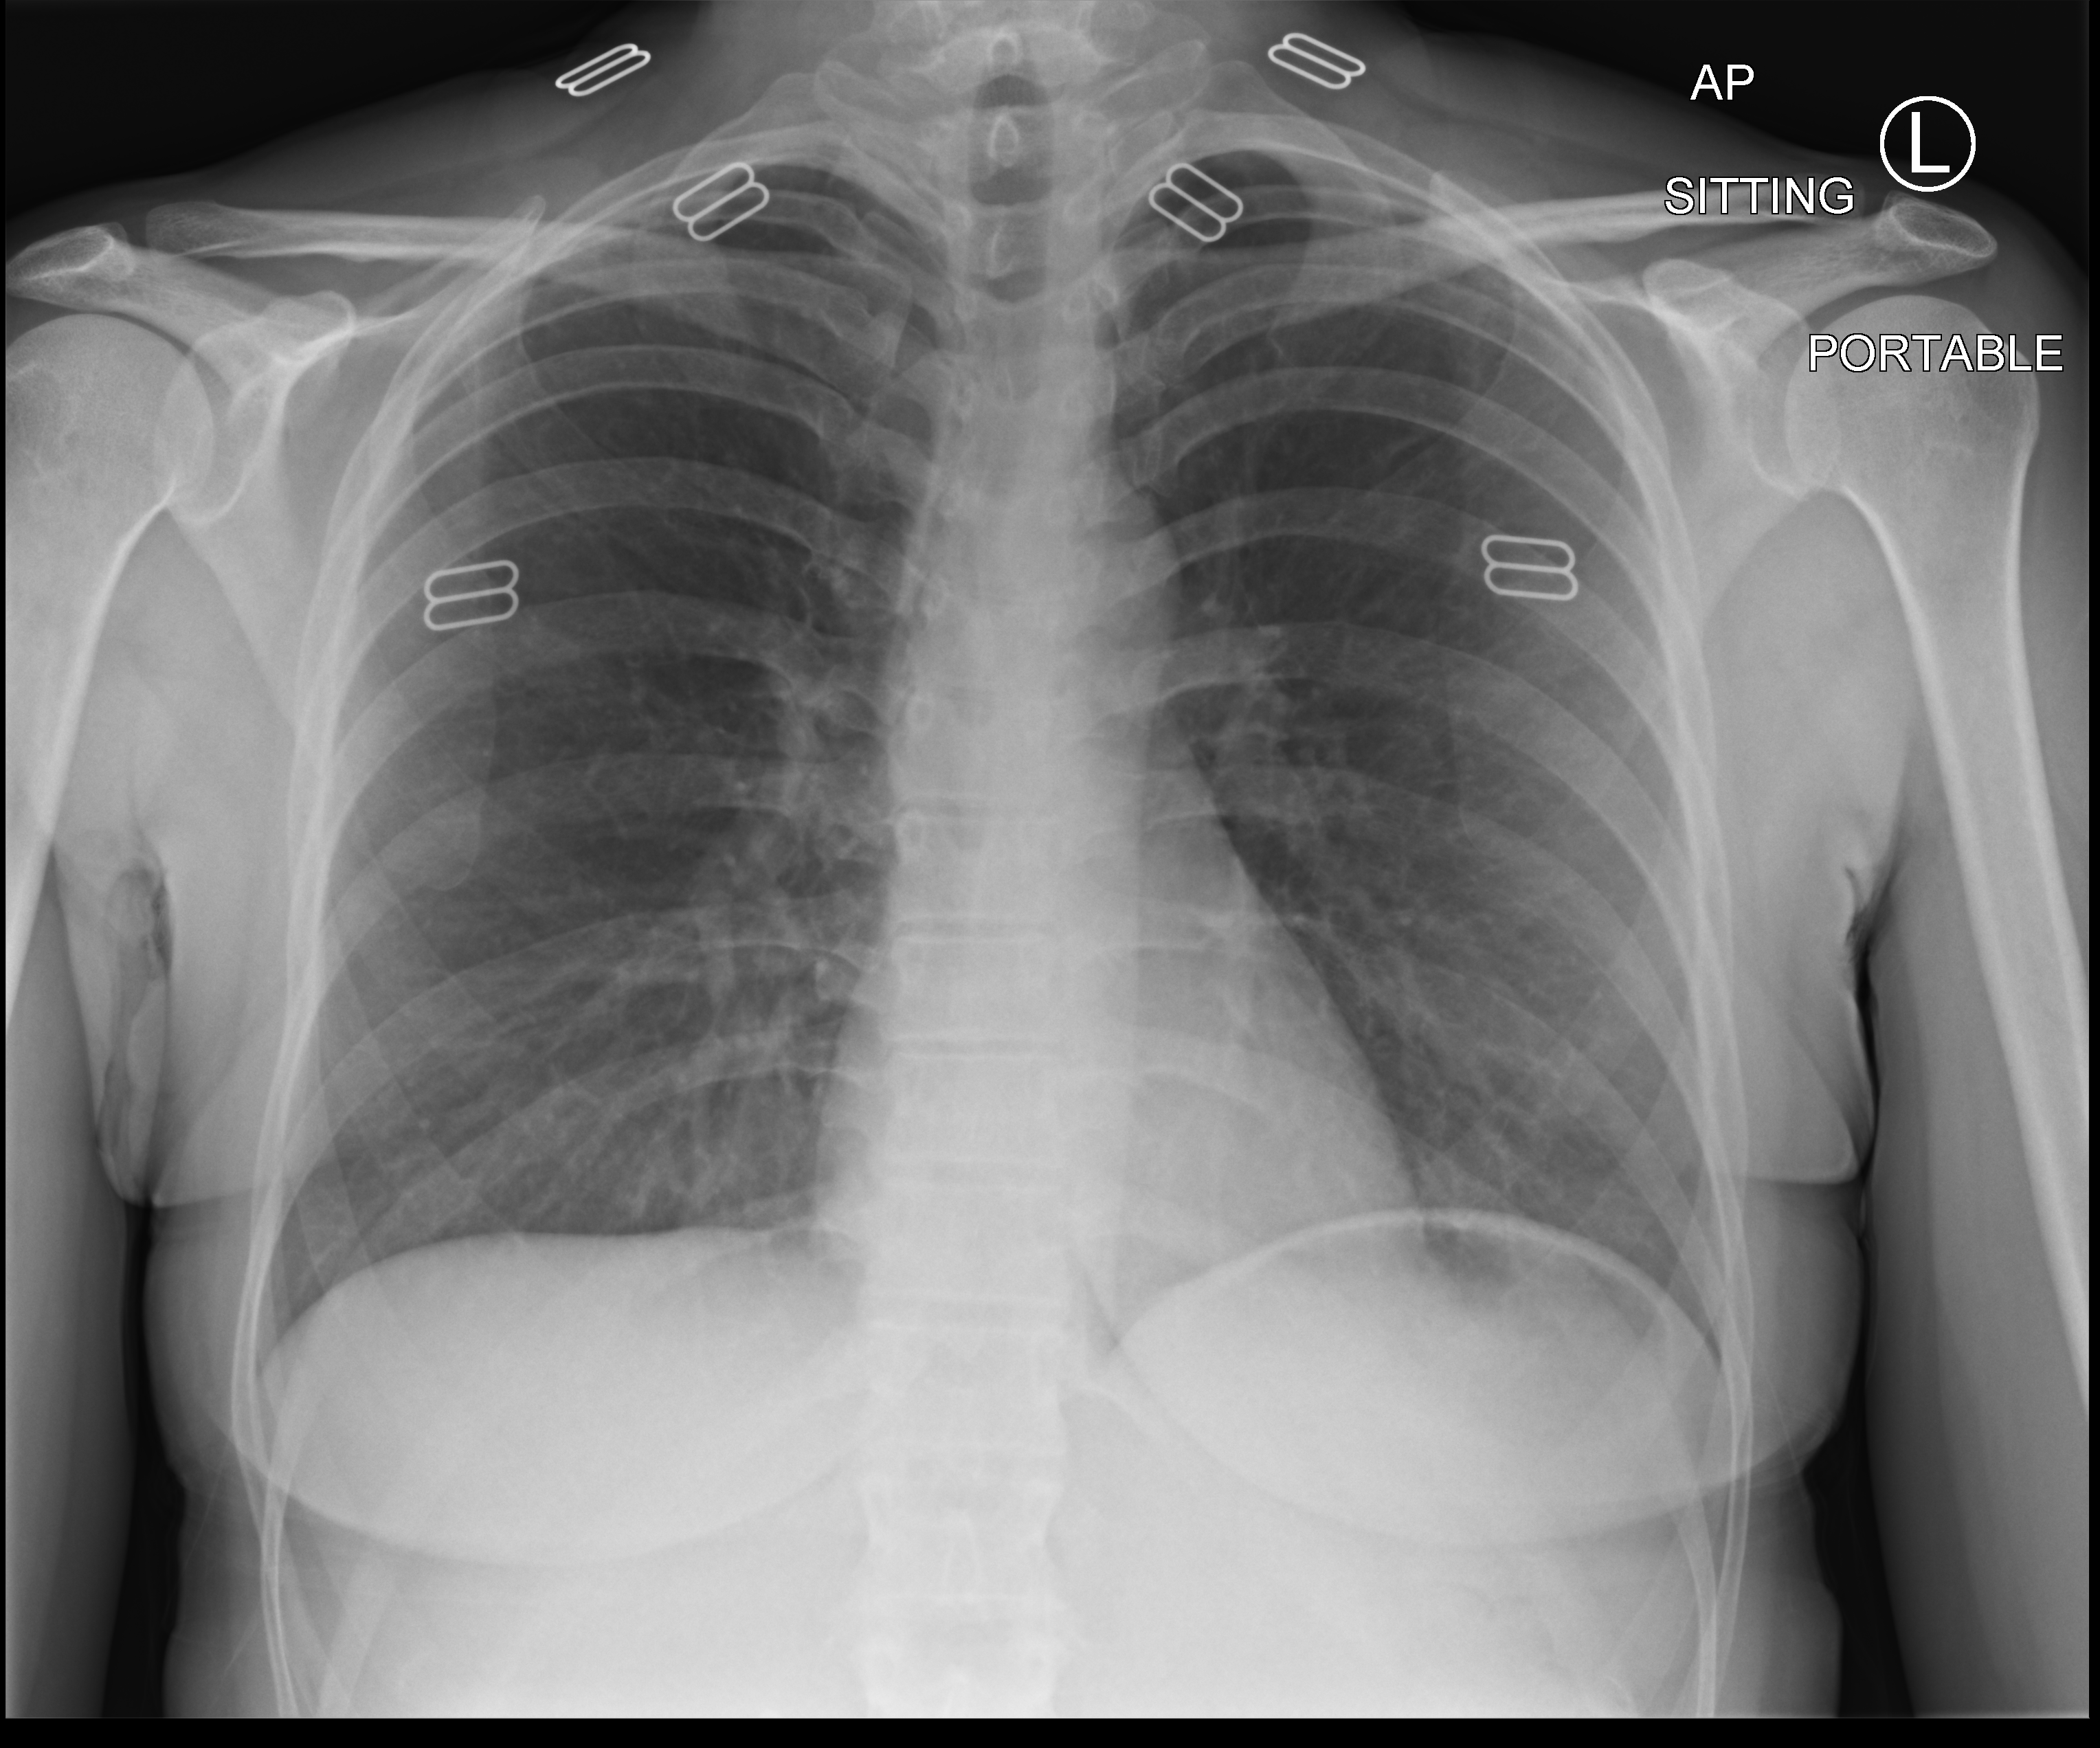
Chest X-ray (portable); anteroposterior (AP) projection. Female patient hospitalised with COVID-19, age 18–59 years.
Hospital-stay facts (about this admission, not read from this image; timing relative to this image not recorded):
- mechanically ventilated during this hospital stay: no
- admitted to intensive care during this hospital stay: no